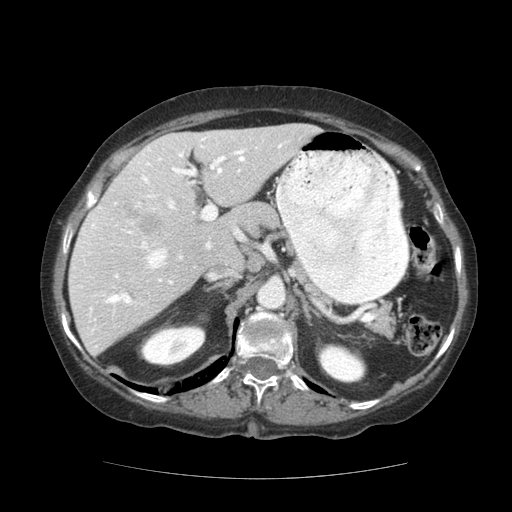
Contrast-enhanced abdominal CT (liver protocol), one axial slice. Slice 75 of 111 in the series (ordered by position). 140 kVp. Soft-tissue window (W 400 / L 40 HU). 2.5 mm slice thickness. 512 × 512 image matrix, field of view 360 × 360 mm. From the clinical record (not read from this slice): diagnosis: hepatocellular carcinoma (patient treated with transarterial chemoembolisation; whether this scan precedes or follows treatment is not stated here); TNM stage (as recorded): Stage-I; Child-Pugh class: A; tumour nodularity: uninodular; tumour size: 7.3 cm.
Annotated regions visible in this slice (semi-automatic segmentation, software-assisted and operator-edited):
- liver parenchyma outside the tumour (the mass and vessels are separate outlines, so this box may not span the whole liver): bounding box (x1, y1, x2, y2) in pixels: (68, 124, 320, 355)
- mass: (123, 202, 162, 236)
- liver vessels: (88, 137, 283, 347)